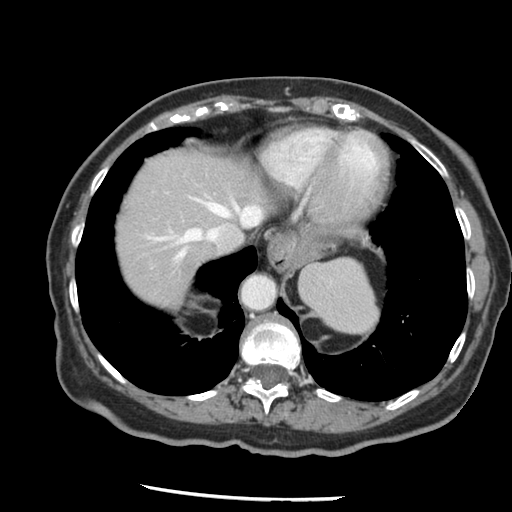
Contrast-enhanced abdominal CT, one axial slice. Position 114 of 148 along the scan axis. 120 kVp. Intravenous contrast given. Soft-tissue window (W 400 / L 40 HU). 2.5 mm slice thickness. 512 × 512 image matrix, field of view 330 × 330 mm. Female patient, age 85 years. Case-level facts recorded for this patient, not image findings: diagnosis: colorectal cancer liver metastases, imaged before liver resection; multiple liver metastases: no; largest metastasis: 0.9 cm; chemotherapy before resection: yes.
Outlined on this slice (expert manual segmentation):
- hepatic veins: bounding box <154,200,261,260> (left, top, right, bottom; pixels)
- liver: <115,148,273,309>
- planned liver remnant (the part of the liver to remain after resection): <115,148,274,309>